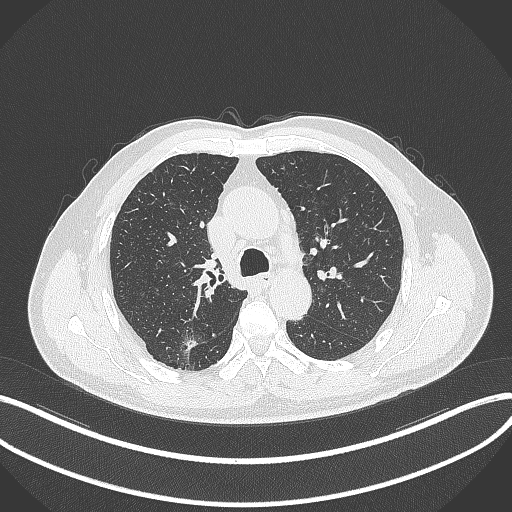
Chest CT, one axial slice; slice 251 of 359 in the series (ordered by position); lung window (W 1500 / L -600 HU); 1 mm slice thickness; 512 × 512 image matrix, field of view 400 × 400 mm. Male patient, age 69 years. Case-level facts recorded for this patient, not image findings: clinical TNM (as recorded): T1b N0 M0; histopathological grade: G2-3.
Outlined on this slice (bounding box drawn by a radiologist):
- lung tumour (recorded histology: adenocarcinoma): bounding box (x1, y1, x2, y2) in pixels: (182, 334, 198, 350)